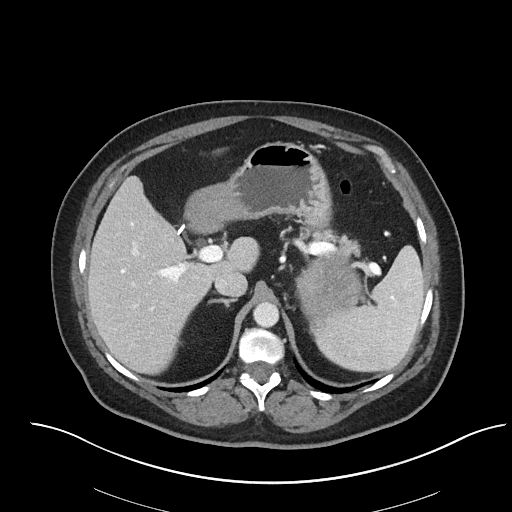
Contrast-enhanced abdominal CT, one axial slice; slice 56 of 92 in the series (ordered by position); reconstruction kernel I40f/2; 120 kVp; intravenous contrast given; soft-tissue window (W 400 / L 40 HU); 3 mm slice thickness; 512 × 512 image matrix, field of view 440 × 440 mm. Patient: female, 53 years. Case-level facts recorded for this patient, not image findings: diagnosis: adrenocortical carcinoma; tumour side: left adrenal; tumour size at pathology: 9 cm; Ki-67 index: 28 %; stage (as recorded): 2.
Annotated regions visible in this slice (semi-automatic segmentation, software-assisted and operator-edited):
- mass: bounding box (x1, y1, x2, y2) in pixels: (297, 259, 359, 323)